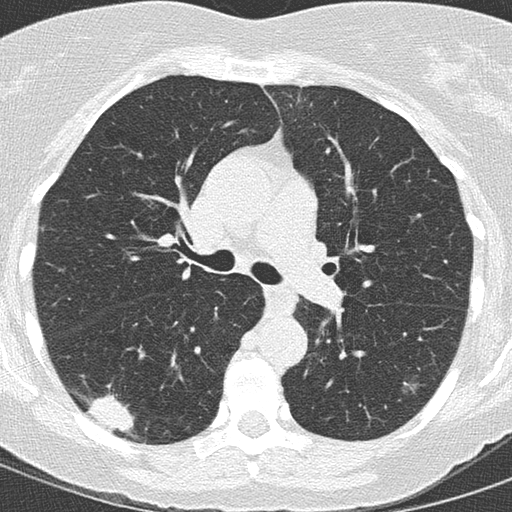
Low-dose screening chest CT, axial slice, baseline screening round, lung window (W 1500 / L -600 HU), lung (sharp) reconstruction kernel (B50f), slice 58 of 146 in the series. Female participant, aged 59 years at enrolment.
• Lesion marked by an expert reader, bounding box [x1, y1, x2, y2] px = [70, 385, 146, 443].
• Reader record for this screening exam (exam-level; its link to the box is not recorded): non-calcified nodule or mass ≥4 mm, right lower lobe, 24 × 15 mm, spiculated (stellate) margins, soft tissue attenuation.
• Official screen result: positive, change unspecified: nodule(s) >= 4 mm or enlarging nodule(s), mass(es), or other non-specific abnormalities suspicious for lung cancer.
• Later outcome: lung cancer diagnosed 12 days after this screen — adenocarcinoma, NOS, right lower lobe, moderately differentiated (G2), stage IIB (AJCC 6th edition), 22 mm at pathology.